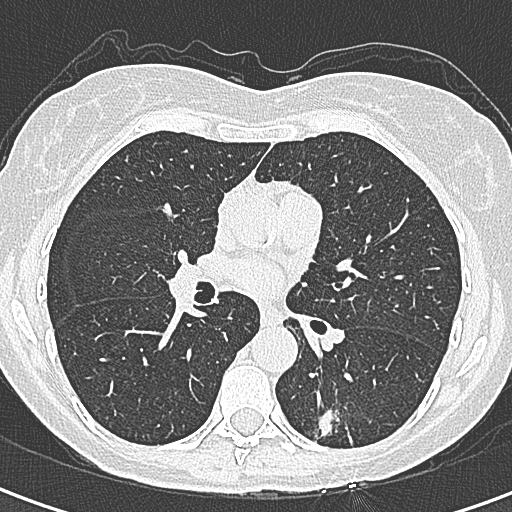
Chest CT (low-dose screening protocol), one axial image. Baseline annual screen. Lung window (W 1500 / L -600 HU). Female, age 58 years at enrolment. Former smoker at enrolment.
- Expert-annotated lung lesion, bounding box [x1, y1, x2, y2] px = [299, 385, 368, 456].
- The screening reader recorded 2 non-calcified nodules or masses ≥4 mm on this exam; which of them this box marks is not recorded.
- Participant outcome: lung cancer diagnosed 22 days after this screen — adenocarcinoma, NOS, left lower lobe, moderately differentiated (G2), stage IA (AJCC 6th edition), 25 mm at pathology.